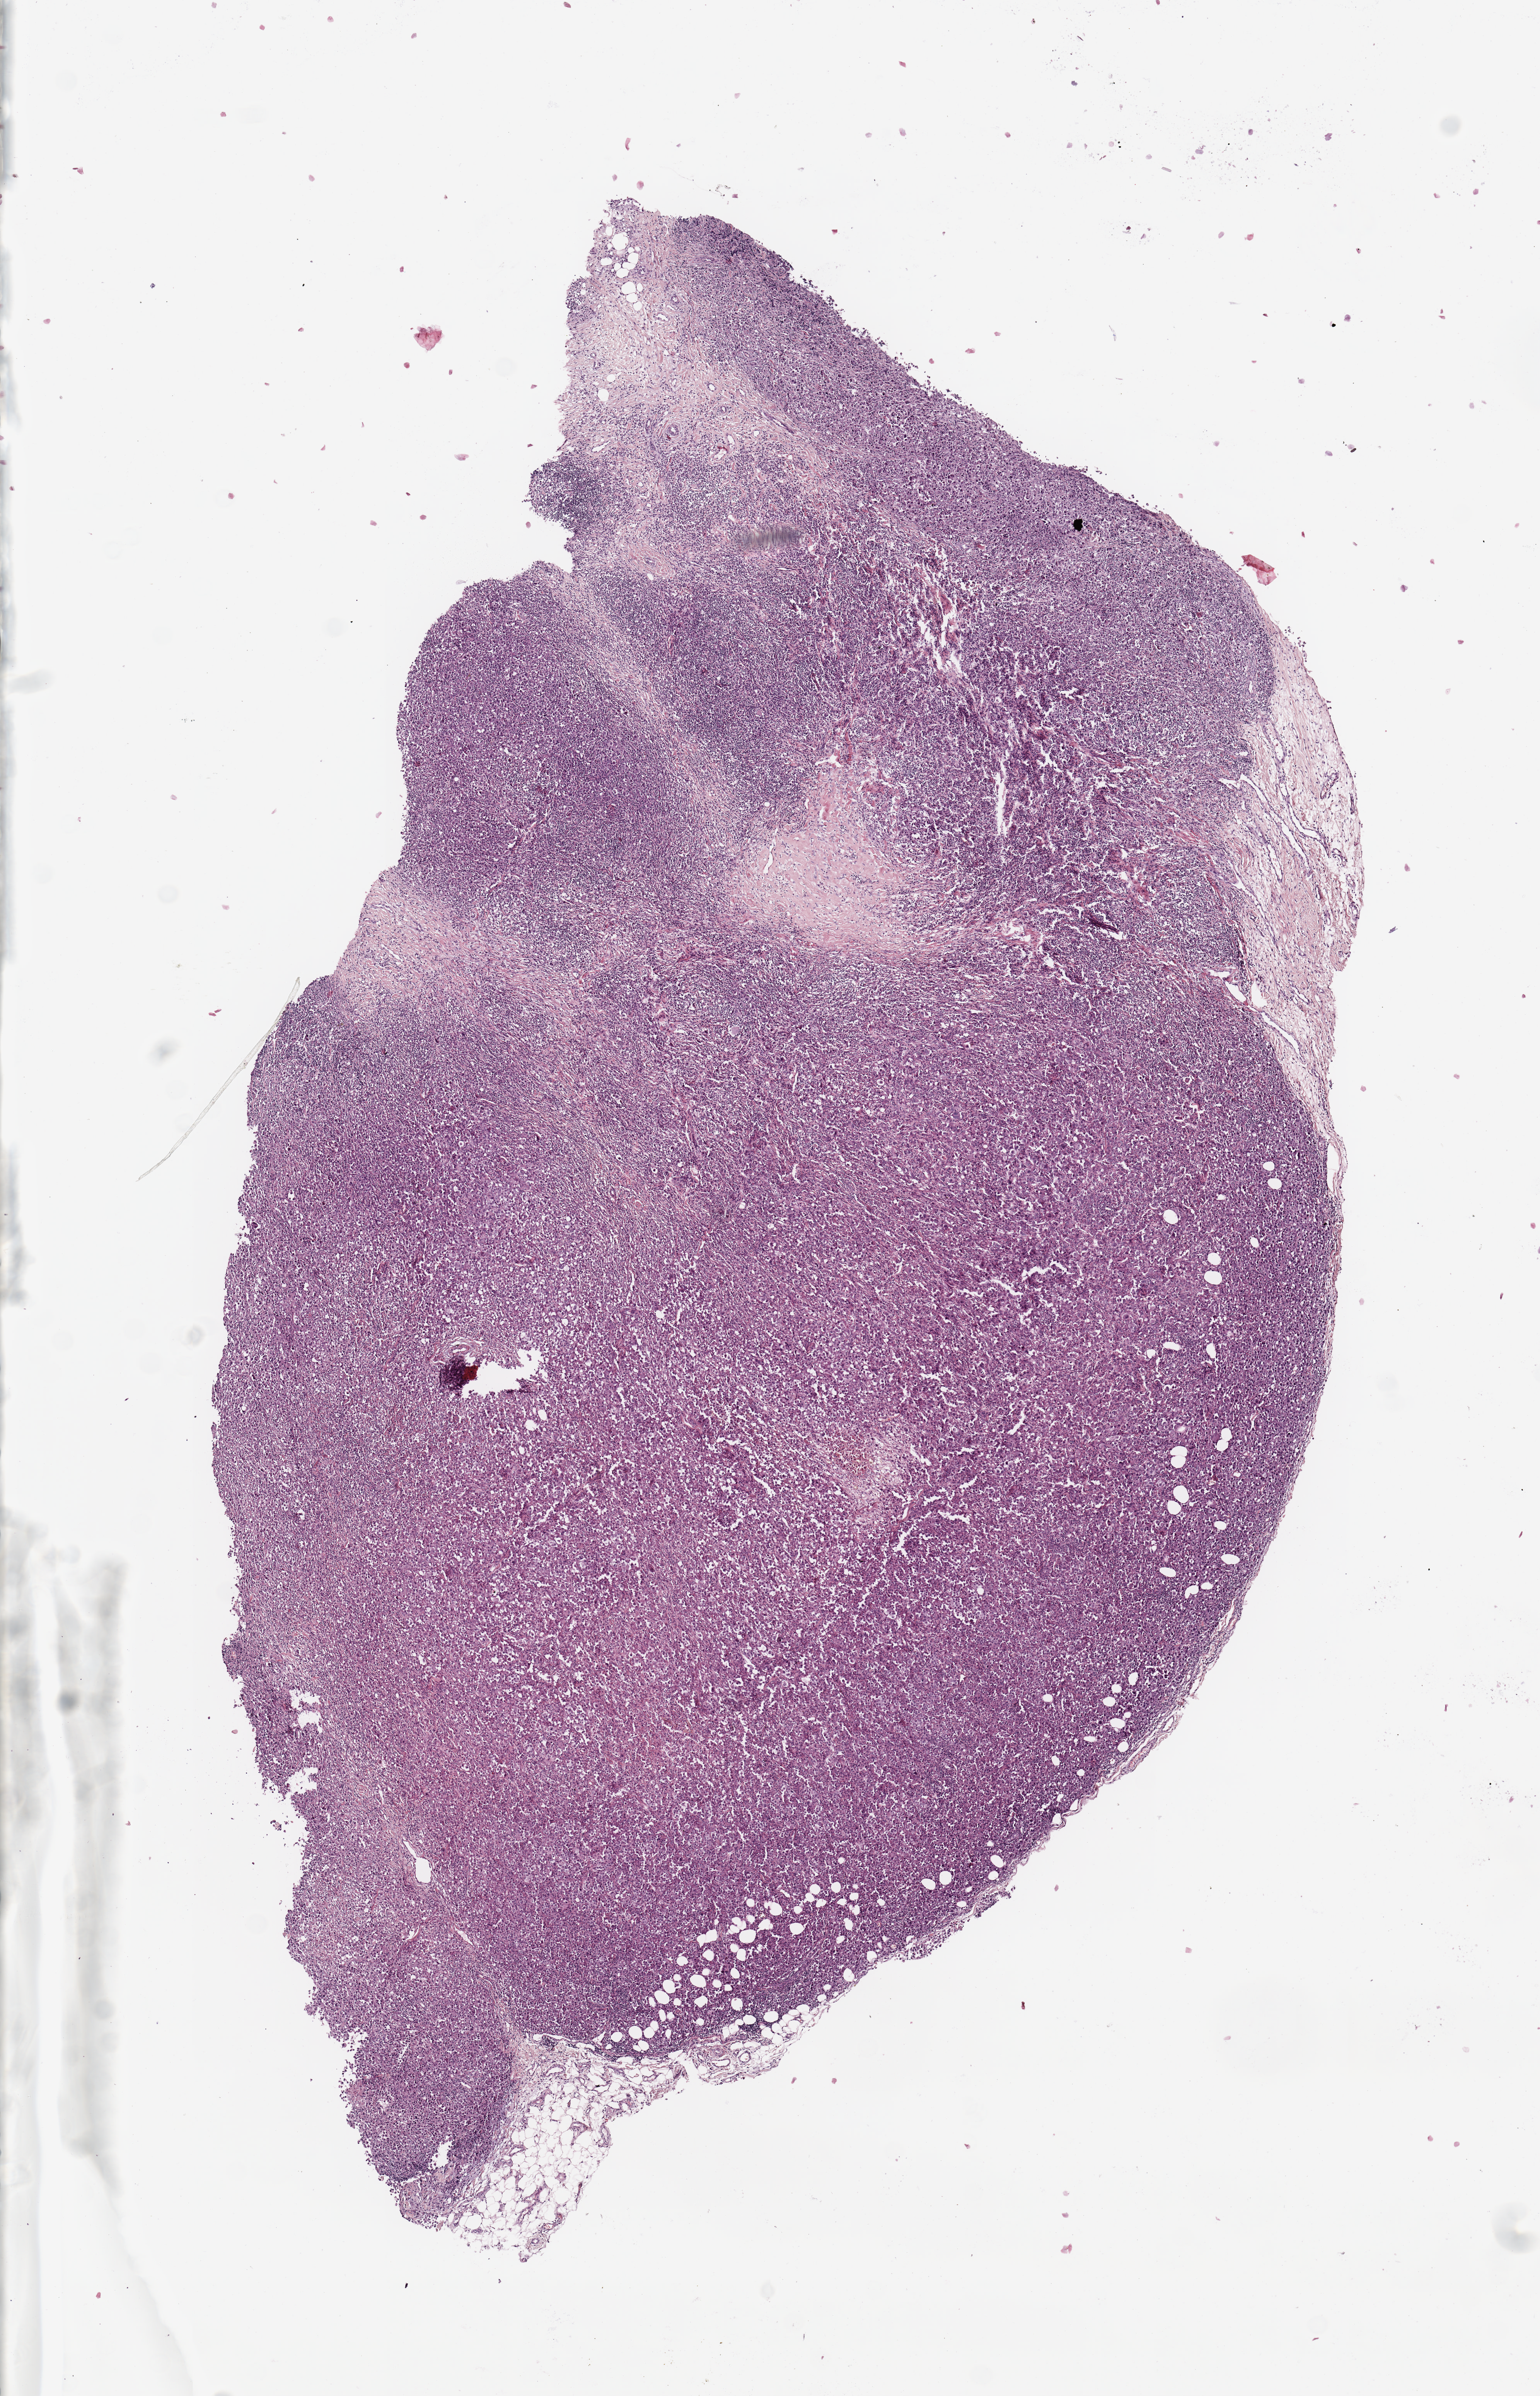
Digitized Hematoxylin and eosin (H&E) stained tissue section (whole slide) — whole scanned area (about 7.9 x 12.3 mm, slide scanned at 20x) shown as a low-resolution overview; melanoma tumour tissue; sampled site not recorded. 76-year-old male patient.
Diagnosis: Malignant melanoma, NOS.